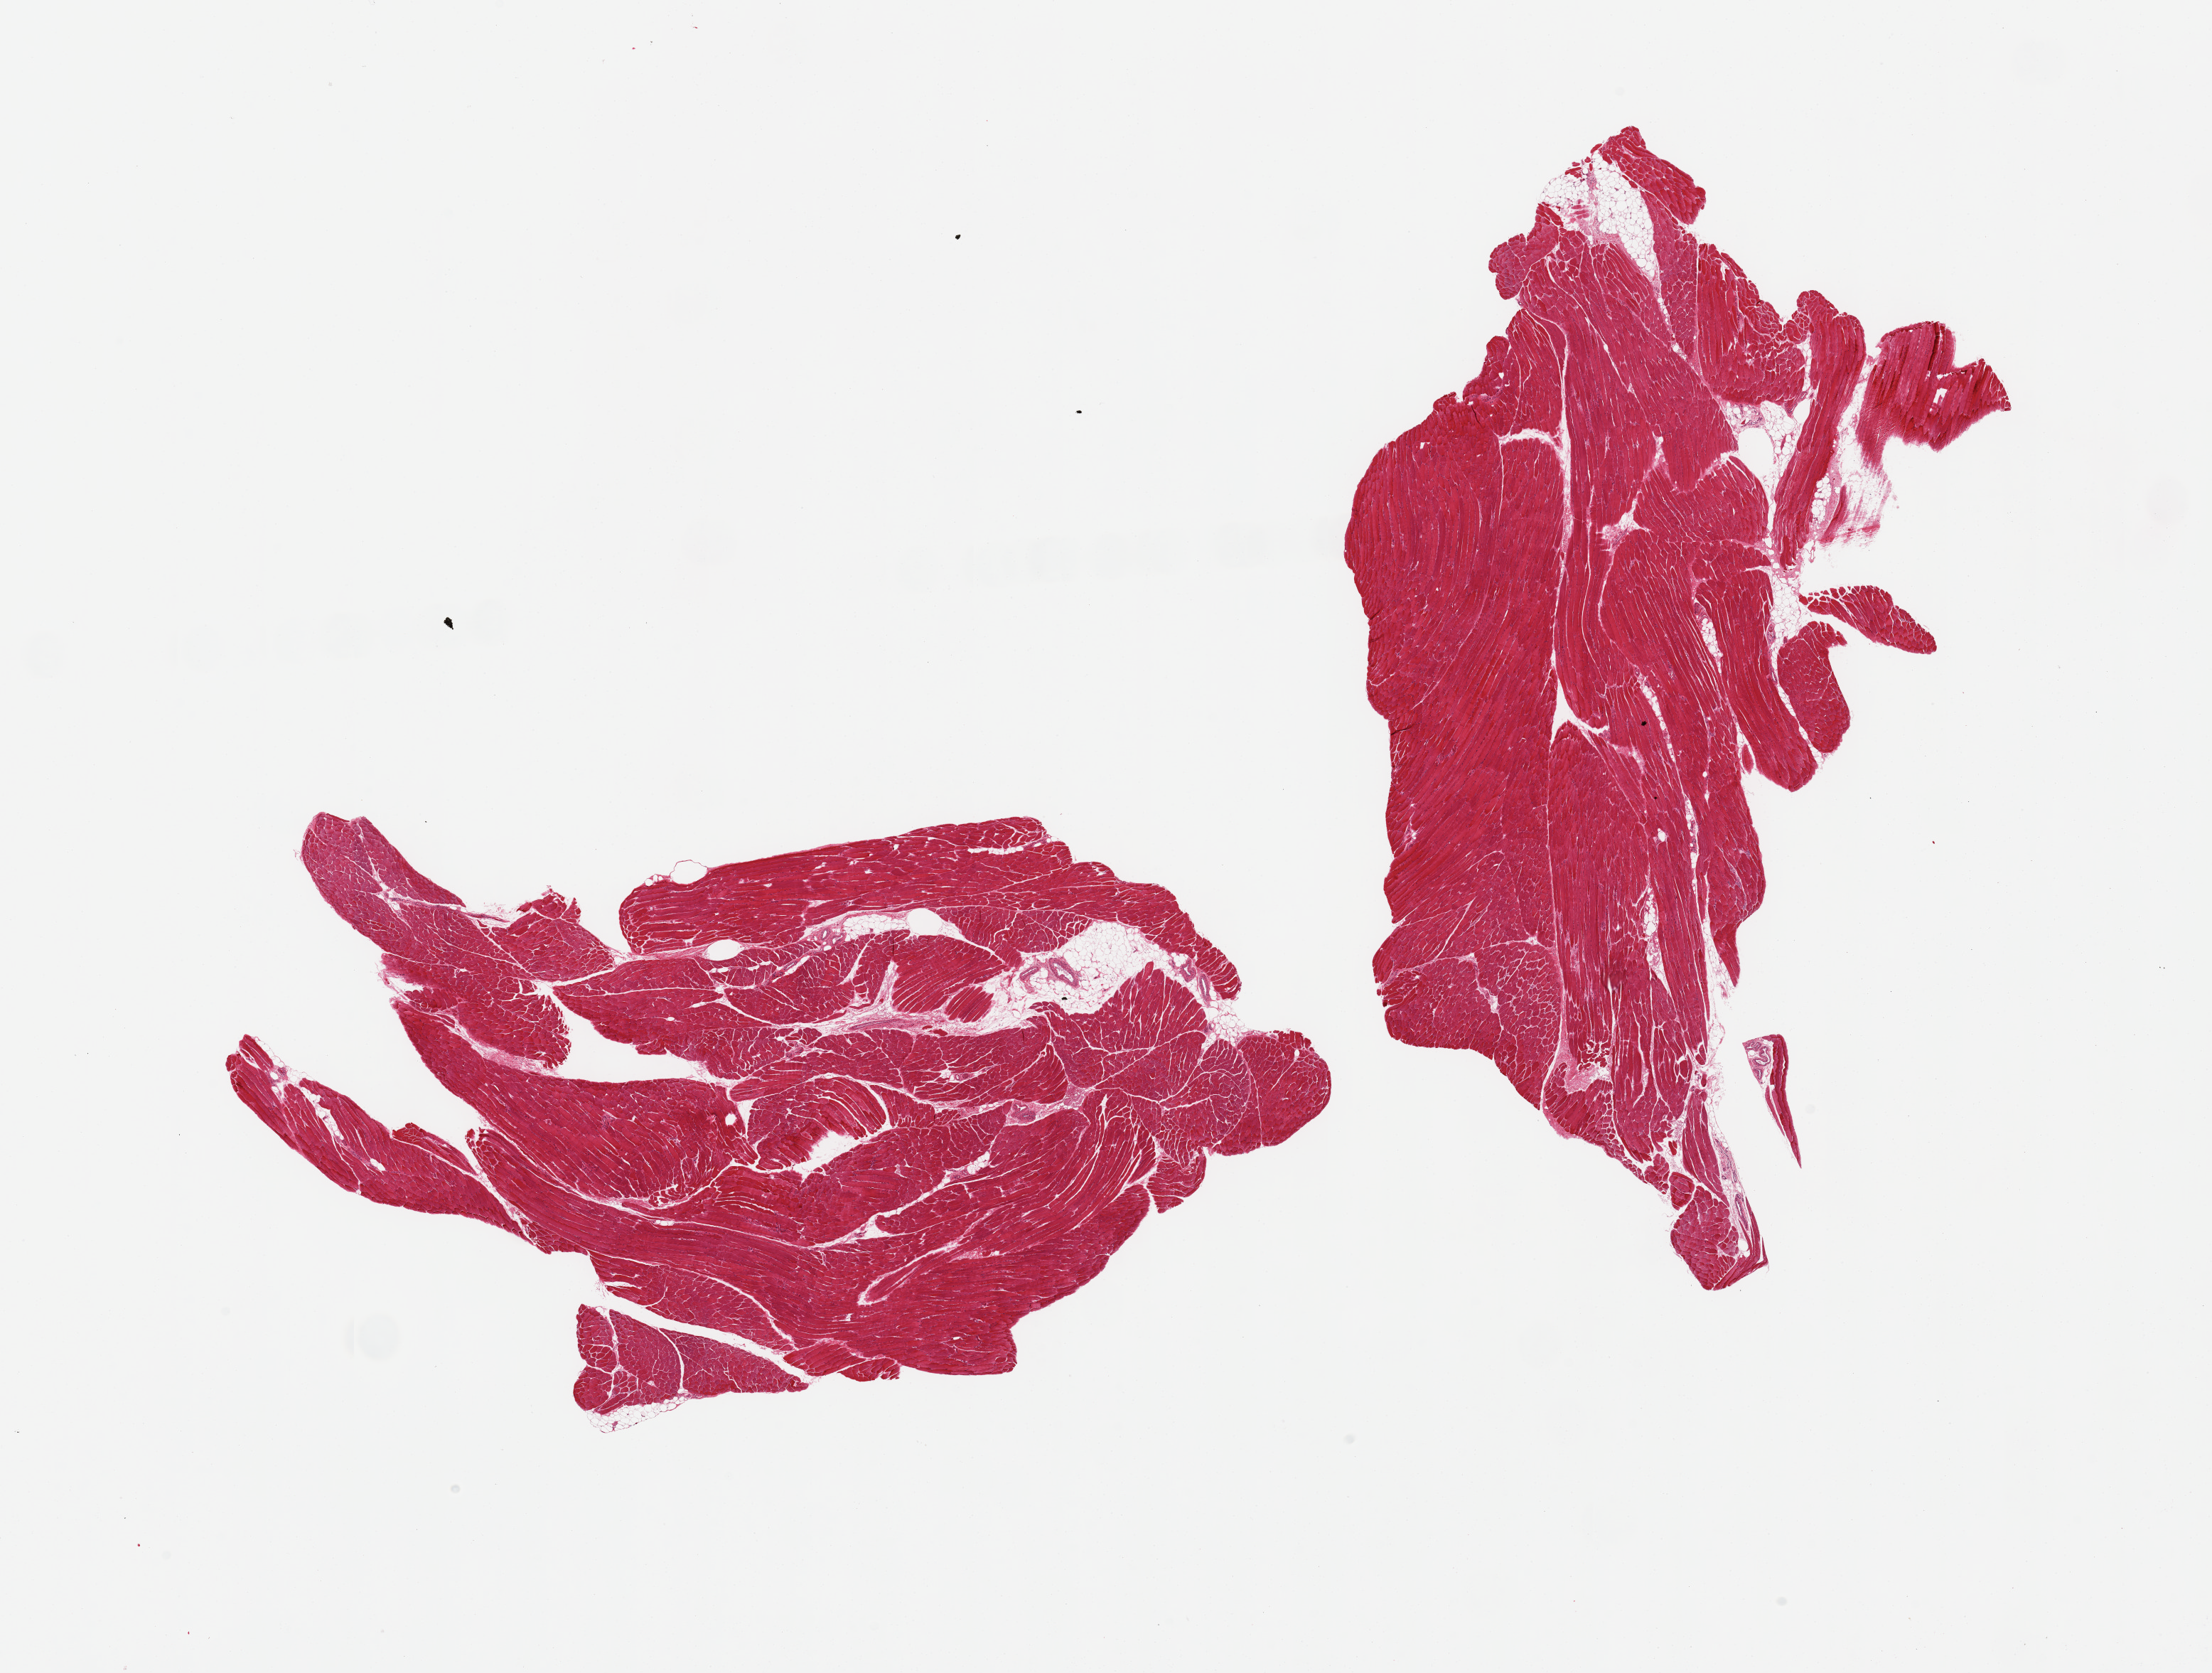
H&E whole-slide image, whole scanned area (about 24.6 x 18.6 mm, from a 20x scan) shown as a low-resolution overview; PAXgene-fixed paraffin-embedded (PFPE) section; section of skeletal muscle (target tissue); donor tissue sample. Donor: male.
Pathologist's review note for this sample: 2 pieces; minimal internal fat.